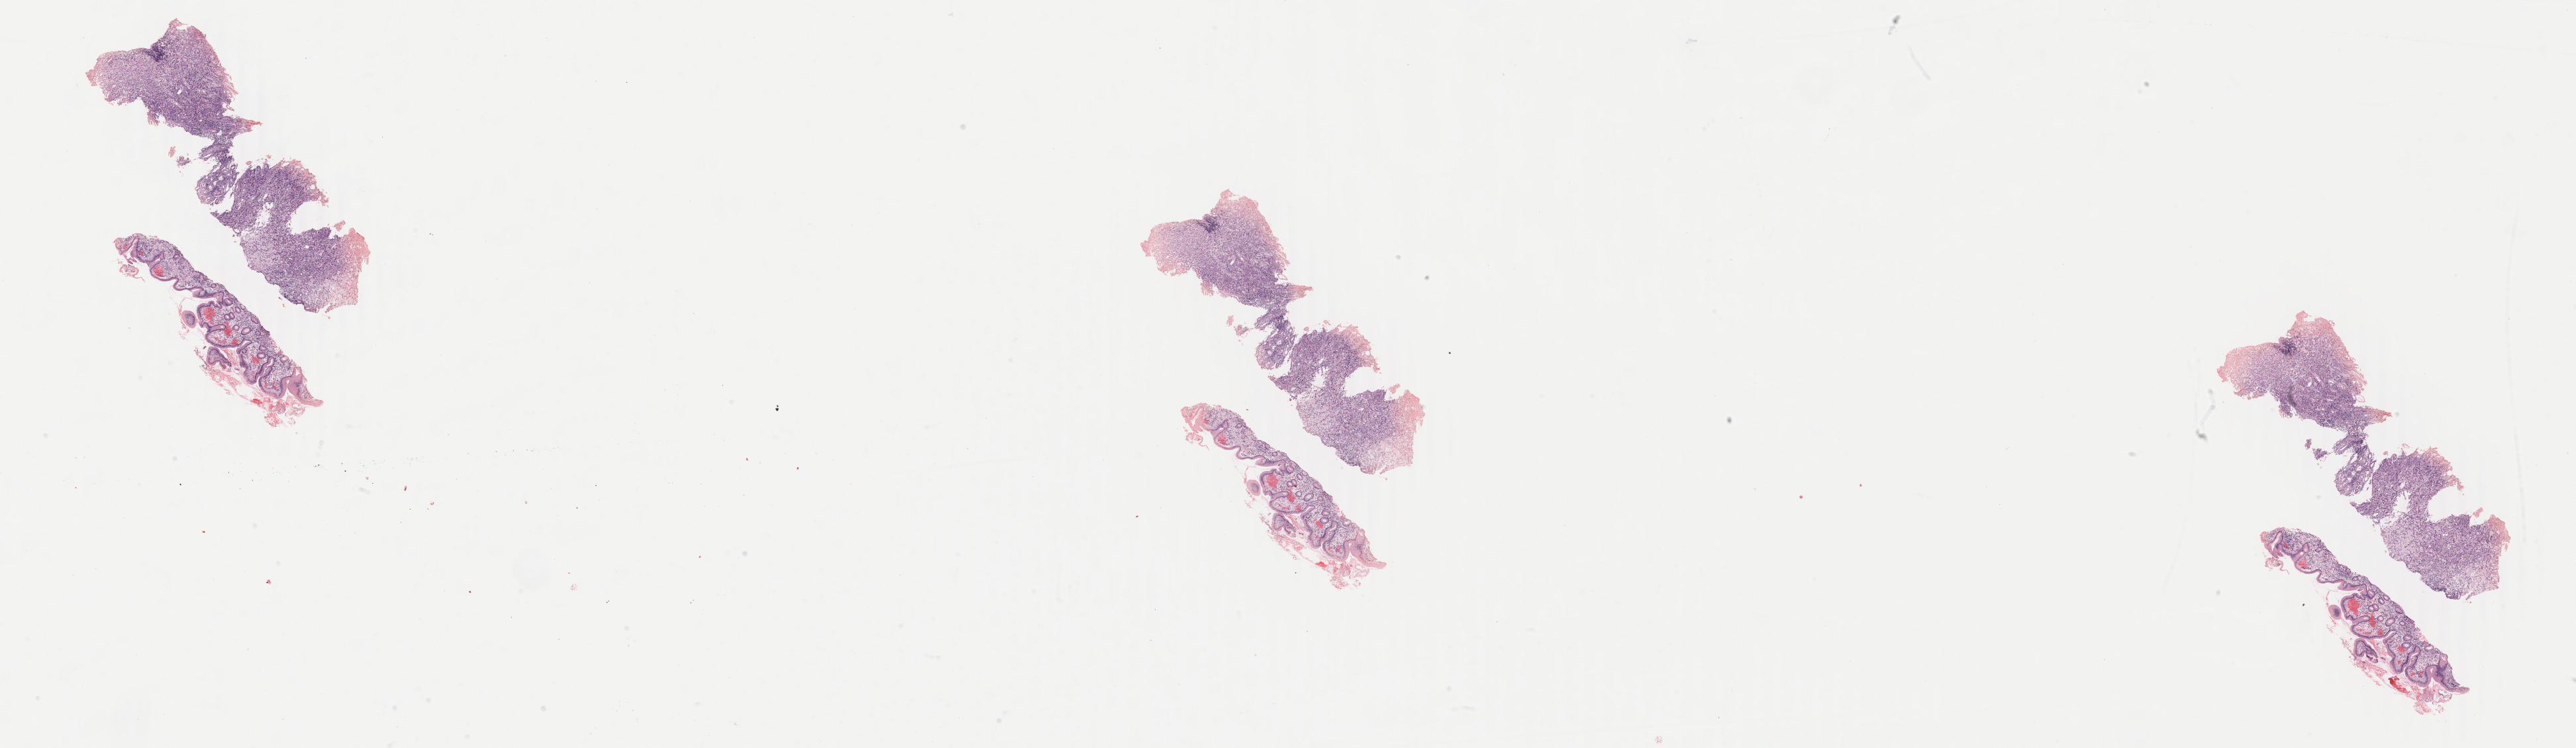
Digitized H&E-stained tissue section (whole slide) — low-resolution overview of the scanned area, about 30.9 x 9.0 mm (acquisition: 40x scan), formalin-fixed paraffin-embedded (FFPE) diagnostic section, sample: primary tumour, stomach. Male, age 54 years at initial diagnosis. Histologic grade: G3 (poorly differentiated). Slide review estimates, as recorded: tumour cells 75%, tumour nuclei 75%, normal cells 9%, stromal cells 14%, necrosis 2%. Inflammatory infiltration, as recorded: lymphocyte infiltration 2%, monocyte infiltration 1%, neutrophil infiltration 4%.
Pathologic diagnosis: Carcinoma, diffuse type. TNM: T3 N2 M1. AJCC pathologic stage: IV (6th edition).